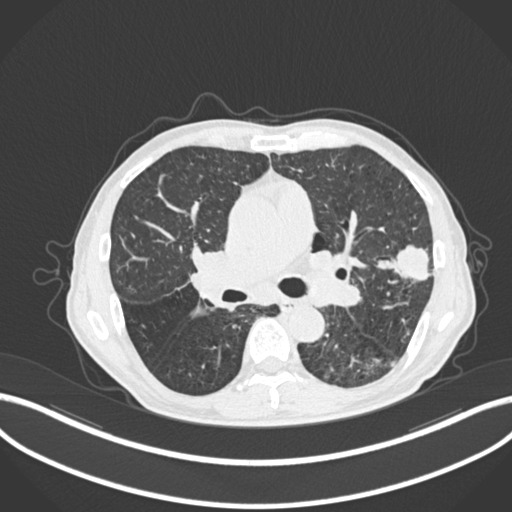
Chest CT, one axial slice; position 141 of 287 along the scan axis; reconstruction kernel B30f; 120 kVp; lung window (W 1500 / L -600 HU); 1 mm slice thickness; 512 × 512 image matrix, field of view 400 × 400 mm. Patient: male, 74 years. Case-level facts recorded for this patient, not image findings: clinical TNM (as recorded): T2a N1 M0.
Structures marked on this image (rectangle marked by the reading radiologist):
- lung tumour (recorded histology: adenocarcinoma): bounding box (x1, y1, x2, y2) in pixels: (375, 246, 433, 286)